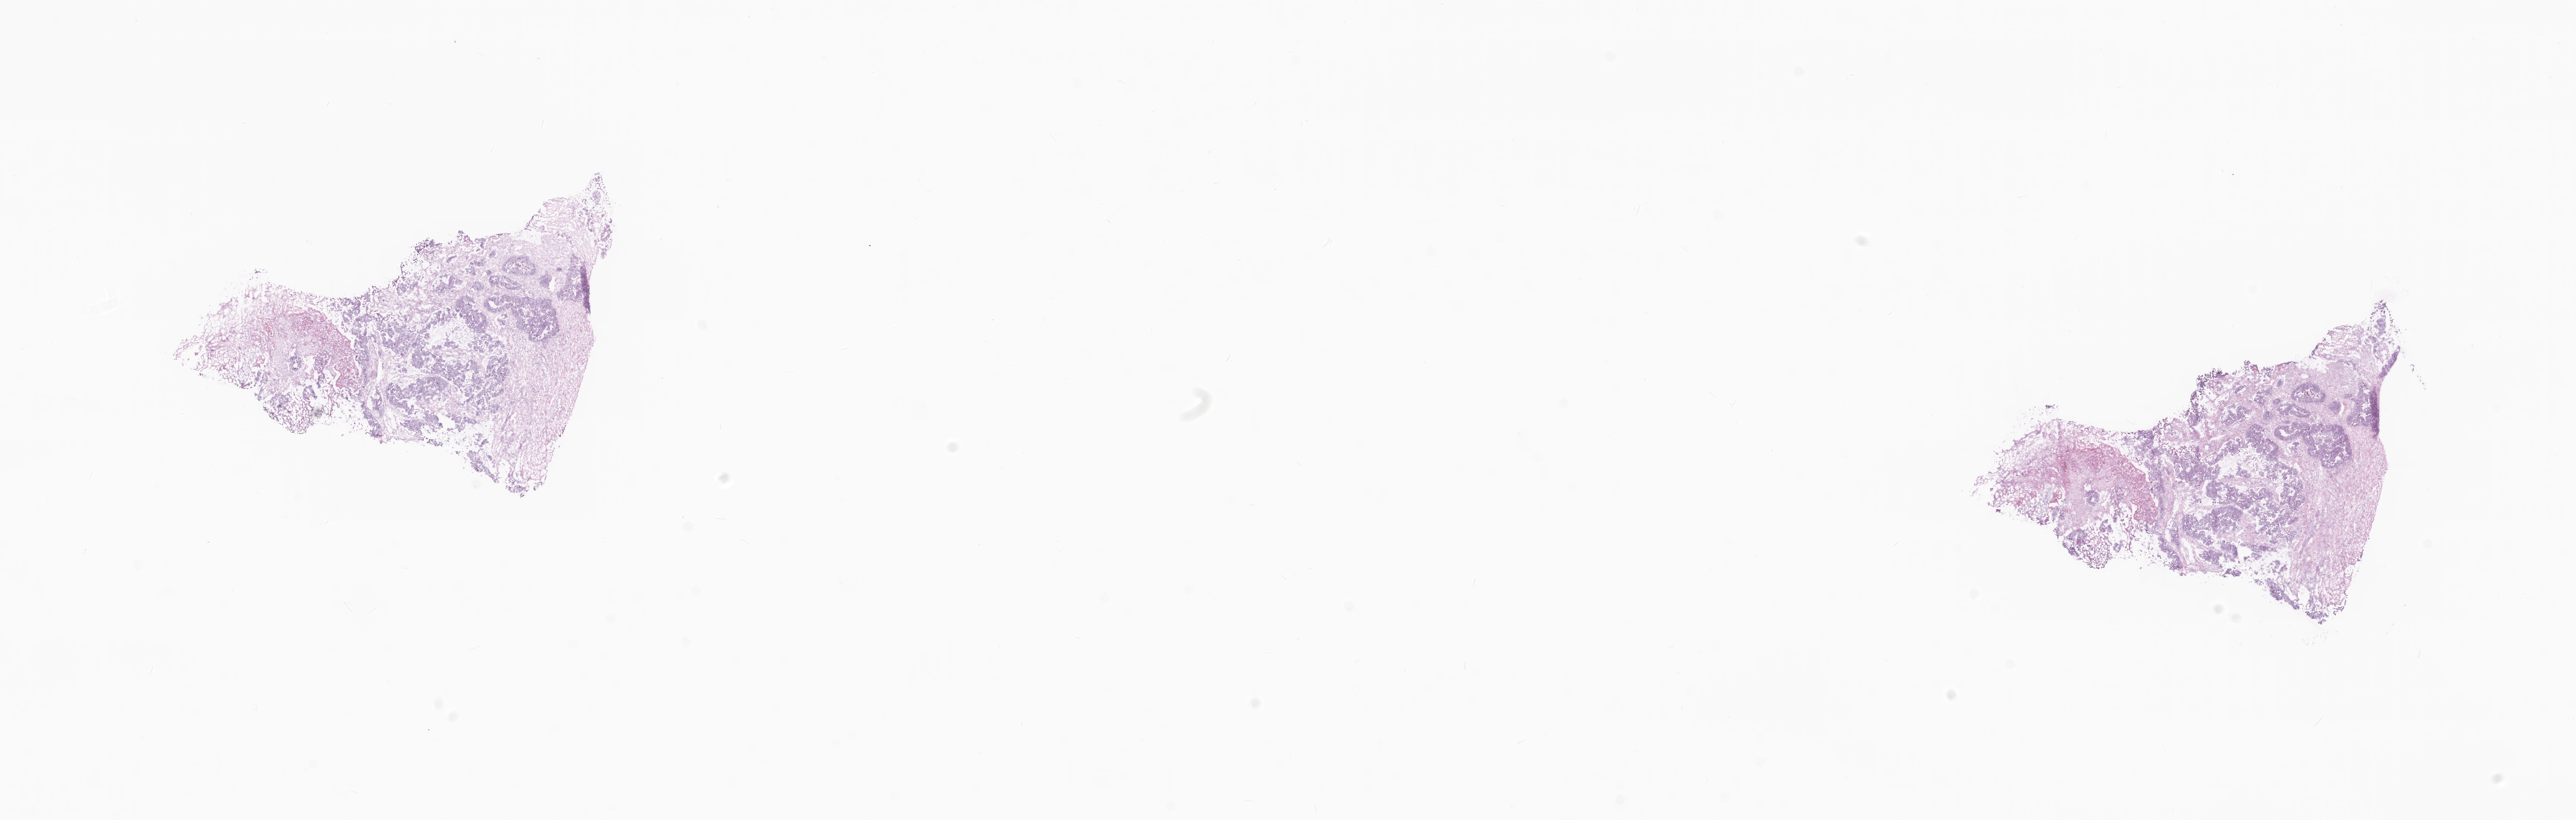
Haematoxylin and eosin whole-slide image, whole scanned area (about 27.5 x 8.8 mm) shown as a low-resolution overview; cryosection; specimen: primary tumor; site: ascending colon. Male patient; age at initial diagnosis 76 years. Composition of this section per pathologist review: tumor cells 34%, tumor nuclei 67%, stromal cells 31%, necrosis 18%, normal cells 17%. Inflammatory infiltration, as recorded: lymphocyte infiltration 1%, monocyte infiltration 5%, neutrophil infiltration 0%.
Histologic diagnosis: Adenocarcinoma, NOS. Section: bottom of the tissue portion.